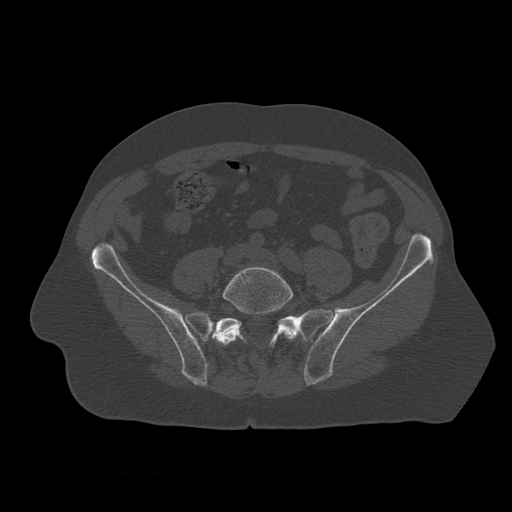
CT including the spine, one axial slice. Position 247 of 450 along the scan axis. 120 kVp. Bone window (W 1800 / L 400 HU). 512 × 512 image matrix, field of view 405 × 405 mm. Patient age 75 years. Case-level facts recorded for this patient, not image findings: primary cancer: prostate.
Outlined on this slice (semi-automatically segmented with operator editing):
- L5 vertebra: bounding box [x1, y1, x2, y2] px = [217, 266, 297, 346]